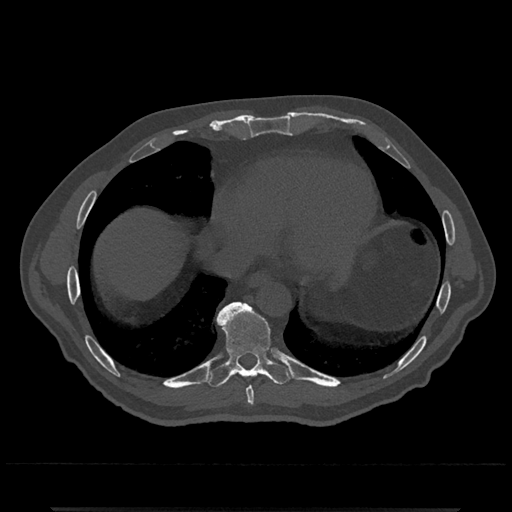
CT including the spine, one axial slice. Position 625 of 797 along the scan axis. Bone window (W 1800 / L 400 HU). 0.5 mm slice thickness. 512 × 512 image matrix, field of view 393 × 393 mm. Male patient, age 67 years. Case-level facts recorded for this patient, not image findings: primary cancer: prostate.
Annotated regions visible in this slice (semi-automatically segmented with operator editing):
- T8 vertebra: bounding box [x1, y1, x2, y2] px = [246, 387, 254, 406]
- T9 vertebra: [206, 302, 293, 388]